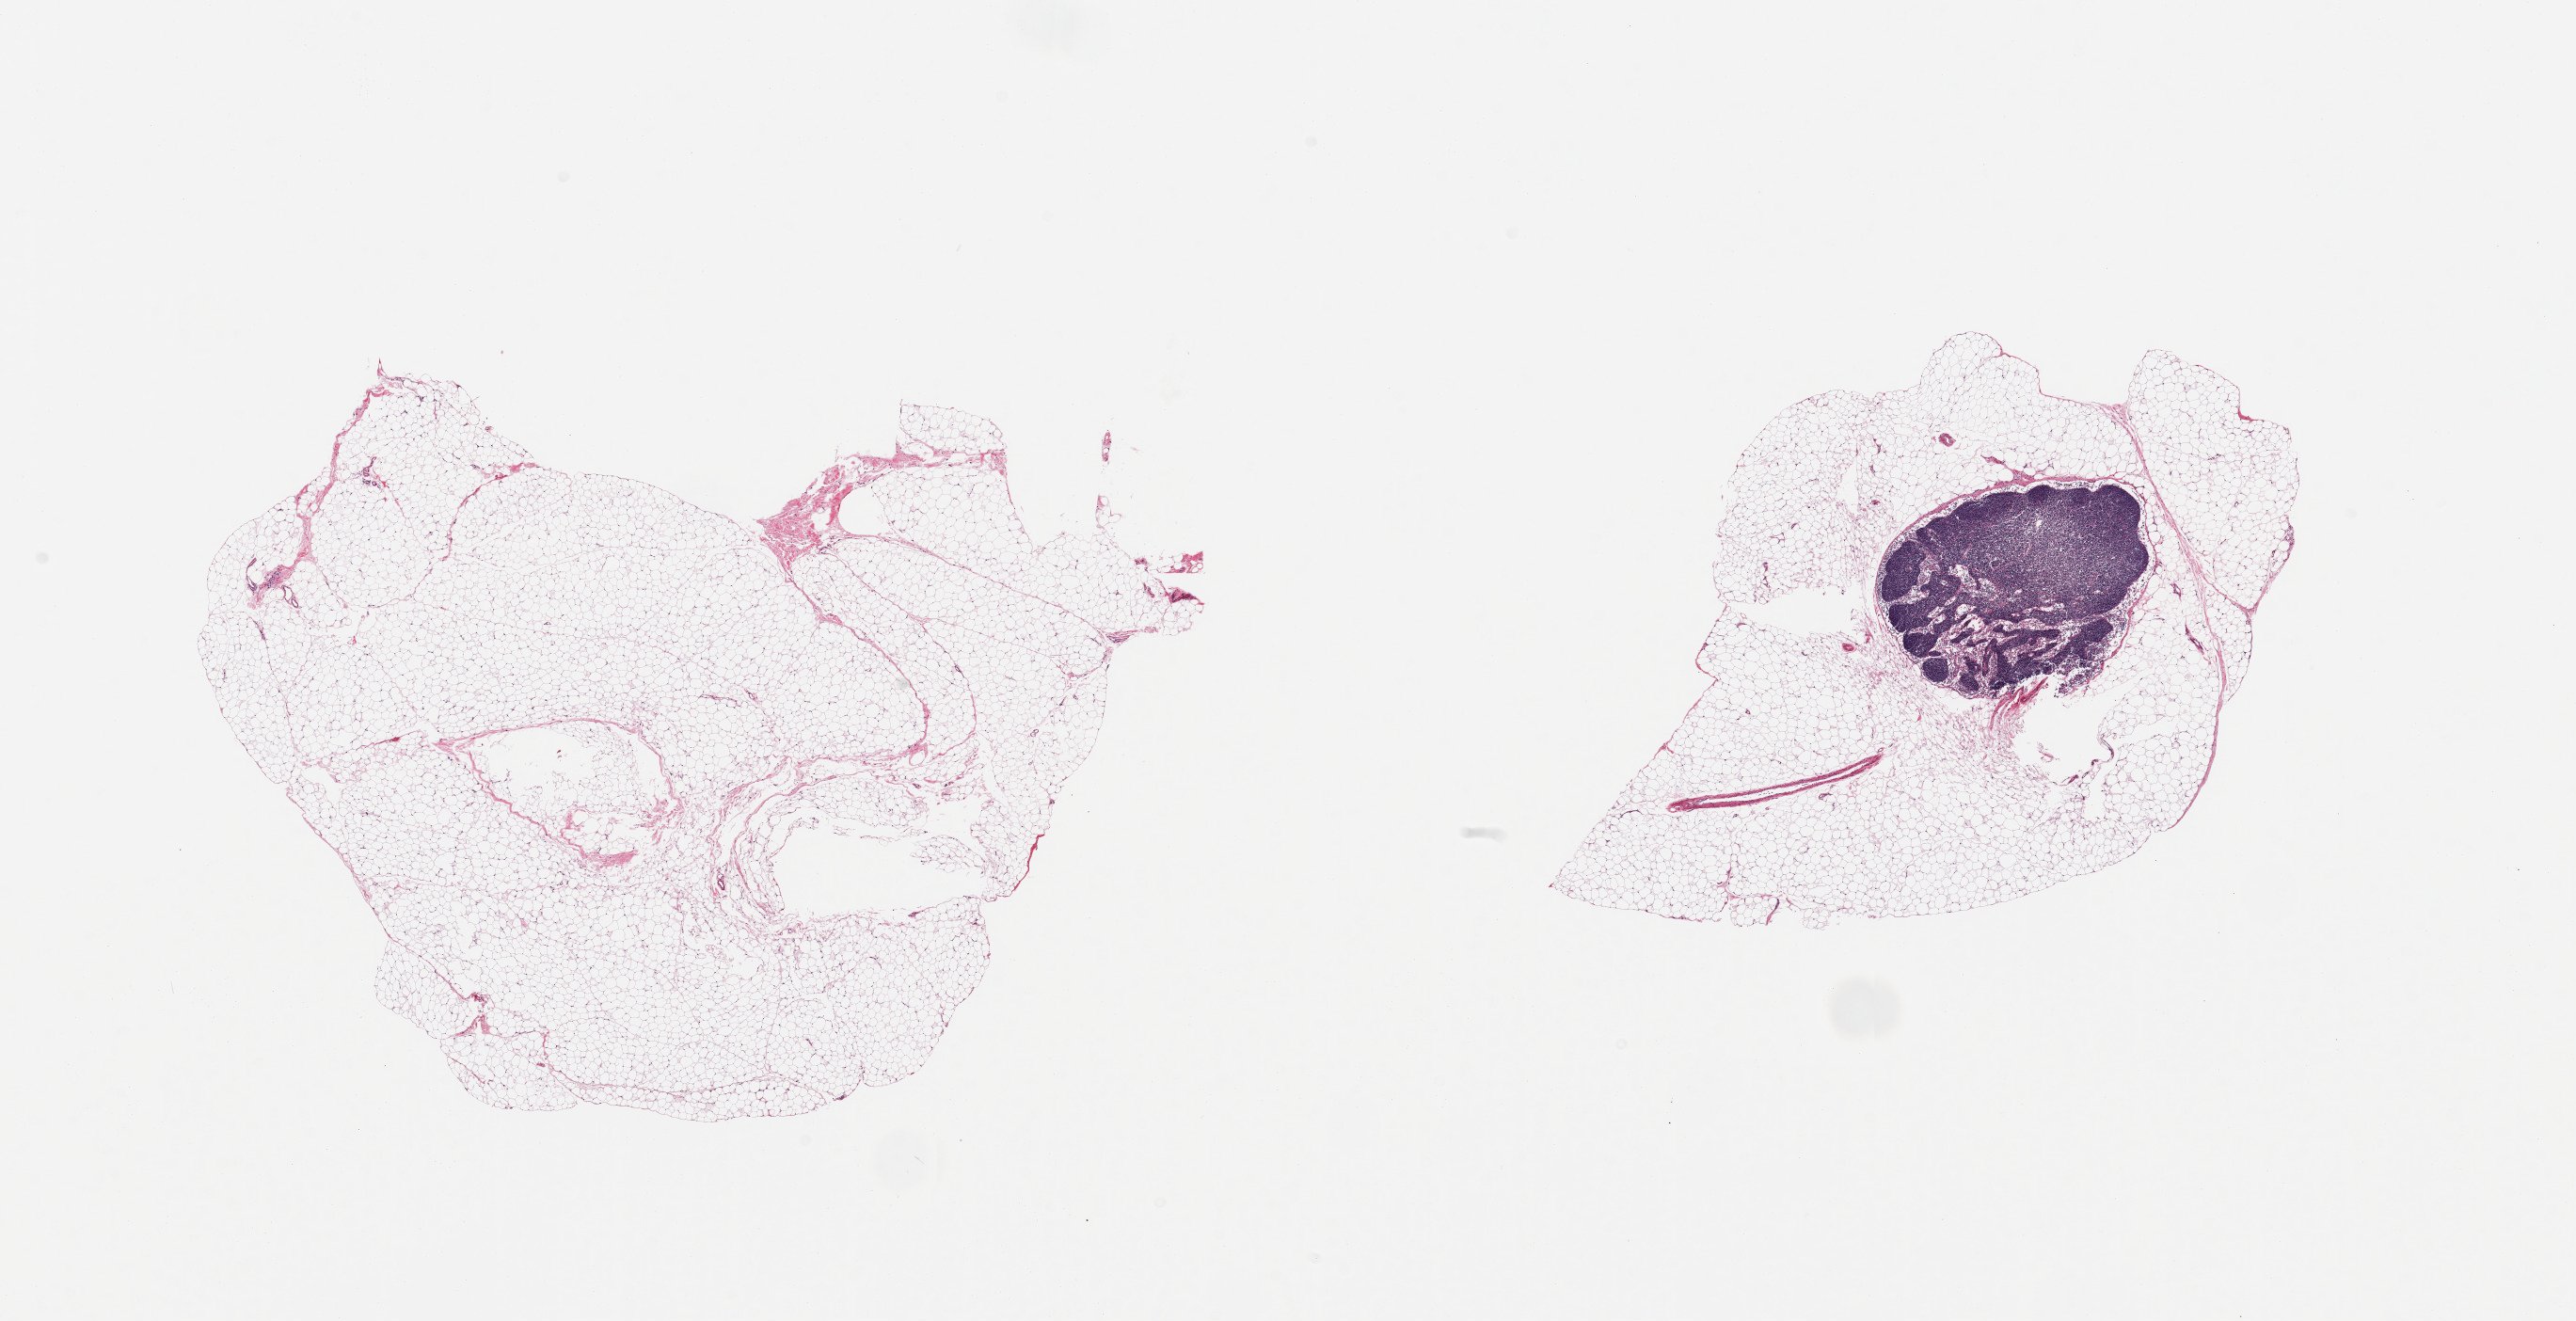
Digitized haematoxylin and eosin-stained section — a low-resolution overview of the entire scanned area, about 21.7 x 11.1 mm, PAXgene-fixed paraffin-embedded (PFPE) section, section of omentum (target tissue), tissue donor sample. Donor sex: female.
Review note (as recorded): 2 pieces; 2 mm lymph node in 1 piece (20%).